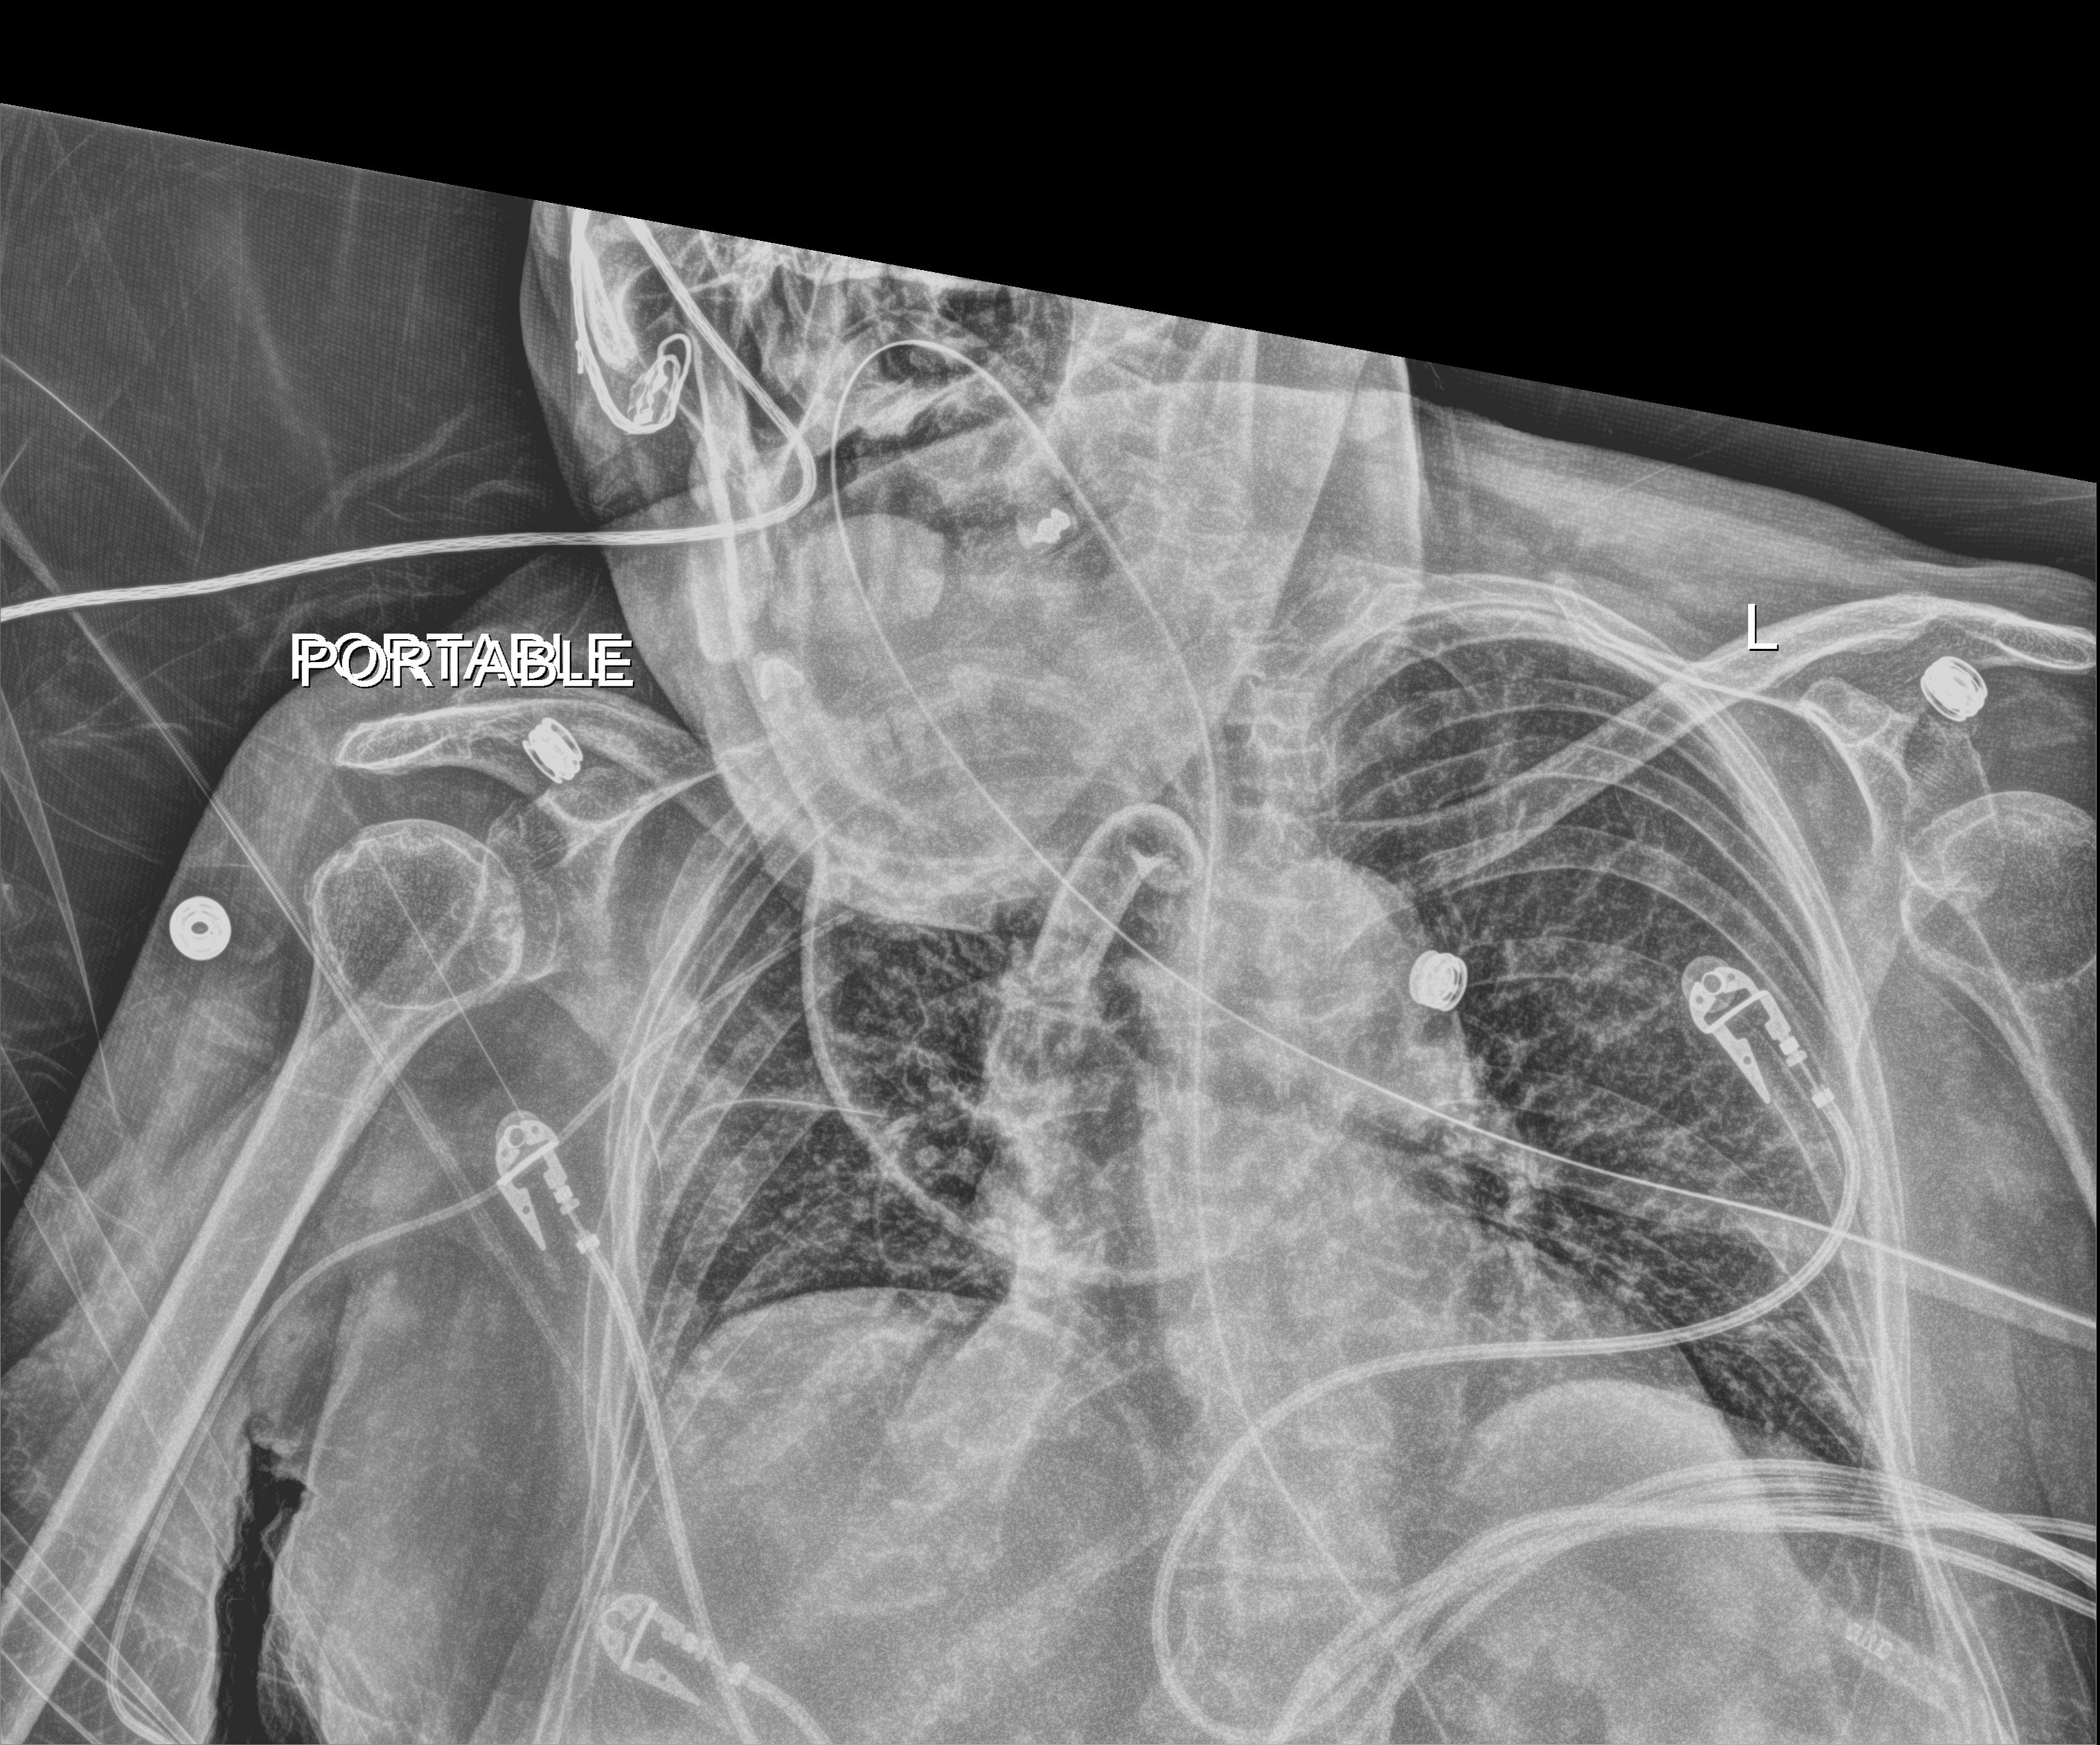
Bedside chest radiograph (digital radiography); anteroposterior (AP) projection. Patient hospitalised with COVID-19; female, aged 75–90 years.
Admission-level facts for this patient (not findings on this image; timing relative to this image not recorded):
- mechanically ventilated during this hospital stay: yes
- admitted to intensive care during this hospital stay: yes
- length of hospital stay: 82 days